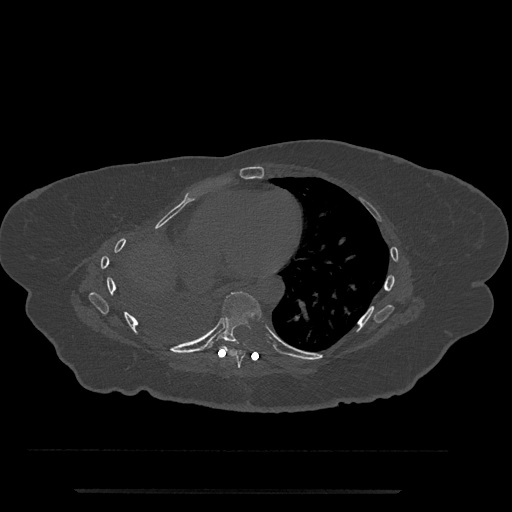
CT including the spine, one axial slice. Position 411 of 797 along the scan axis. Reconstruction kernel Br40s/3. 120 kVp. Bone window (W 1800 / L 400 HU). 0.5 mm slice thickness. 512 × 512 image matrix, field of view 440 × 440 mm. Patient: female, 51 years. Case-level facts recorded for this patient, not image findings: primary cancer: neuro; vertebrae with lytic lesions (as recorded): T8.
Structures marked on this image (semi-automatically segmented with operator editing):
- T7 vertebra: box from (x=224, y=349) to (x=246, y=368) px
- T8 vertebra: (x=207, y=291)–(x=262, y=349)